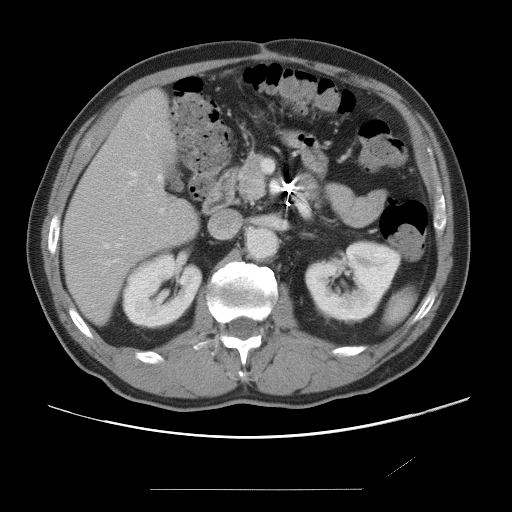
Contrast-enhanced abdominal CT, one axial slice. Intravenous contrast given. Soft-tissue window (W 400 / L 40 HU). 5 mm slice thickness. 512 × 512 image matrix, field of view 406 × 406 mm. Male patient, age 74 years. From the clinical record (not read from this slice): diagnosis: colorectal cancer liver metastases, imaged before liver resection; multiple liver metastases: yes; largest metastasis: 1.1 cm; disease in both lobes: no.
Structures marked on this image (manually delineated by an expert):
- hepatic veins: bounding box <105,136,162,248> (left, top, right, bottom; pixels)
- liver: <66,93,198,323>
- planned liver remnant (the part of the liver to remain after resection): <66,93,198,322>
- portal vein (with intrahepatic branches): <149,189,164,212>